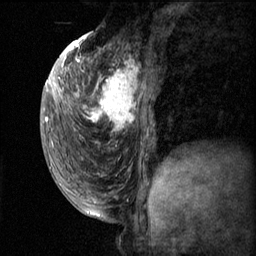
Breast MRI (dynamic contrast-enhanced), one sagittal slice; dynamic contrast-enhanced series, image 2 of 3 at this slice position (ordered by acquisition); 1.5 T; TE 4.2 ms, TR 11.1 ms; 2 mm slice thickness; 256 × 256 image matrix, field of view 180 × 180 mm. Female patient, age 50 years.
Structures marked on this image (semi-automatically segmented with operator editing):
- analysis volume of interest (the breast-tissue region the enhancement analysis was run in; not a lesion): bounding box (x1, y1, x2, y2) in pixels: (82, 56, 158, 143)
- tumour enhancement mask (voxels above the 70 % enhancement threshold inside the analysis volume of interest): (82, 60, 148, 137)